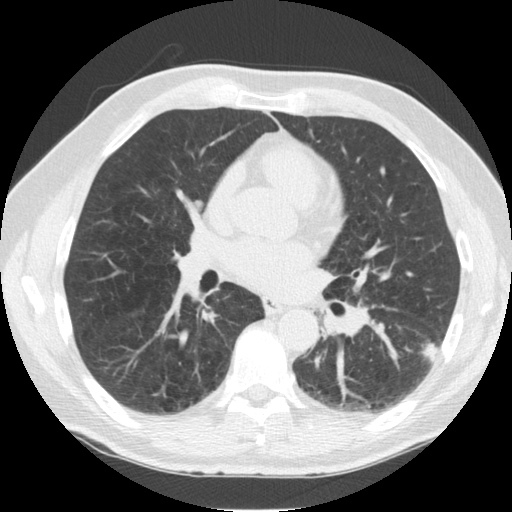
Low-dose screening chest CT, one axial slice; slice 57 of 126 in the series (ordered by position); reconstruction kernel STANDARD; 120 kVp; lung window (W 1500 / L -600 HU); 512 × 512 image matrix.
Outlined on this slice (manually delineated by an expert):
- lesion 1 (tumor, lower lobe of left lung): bounding box <422,342,438,362> (left, top, right, bottom; pixels)